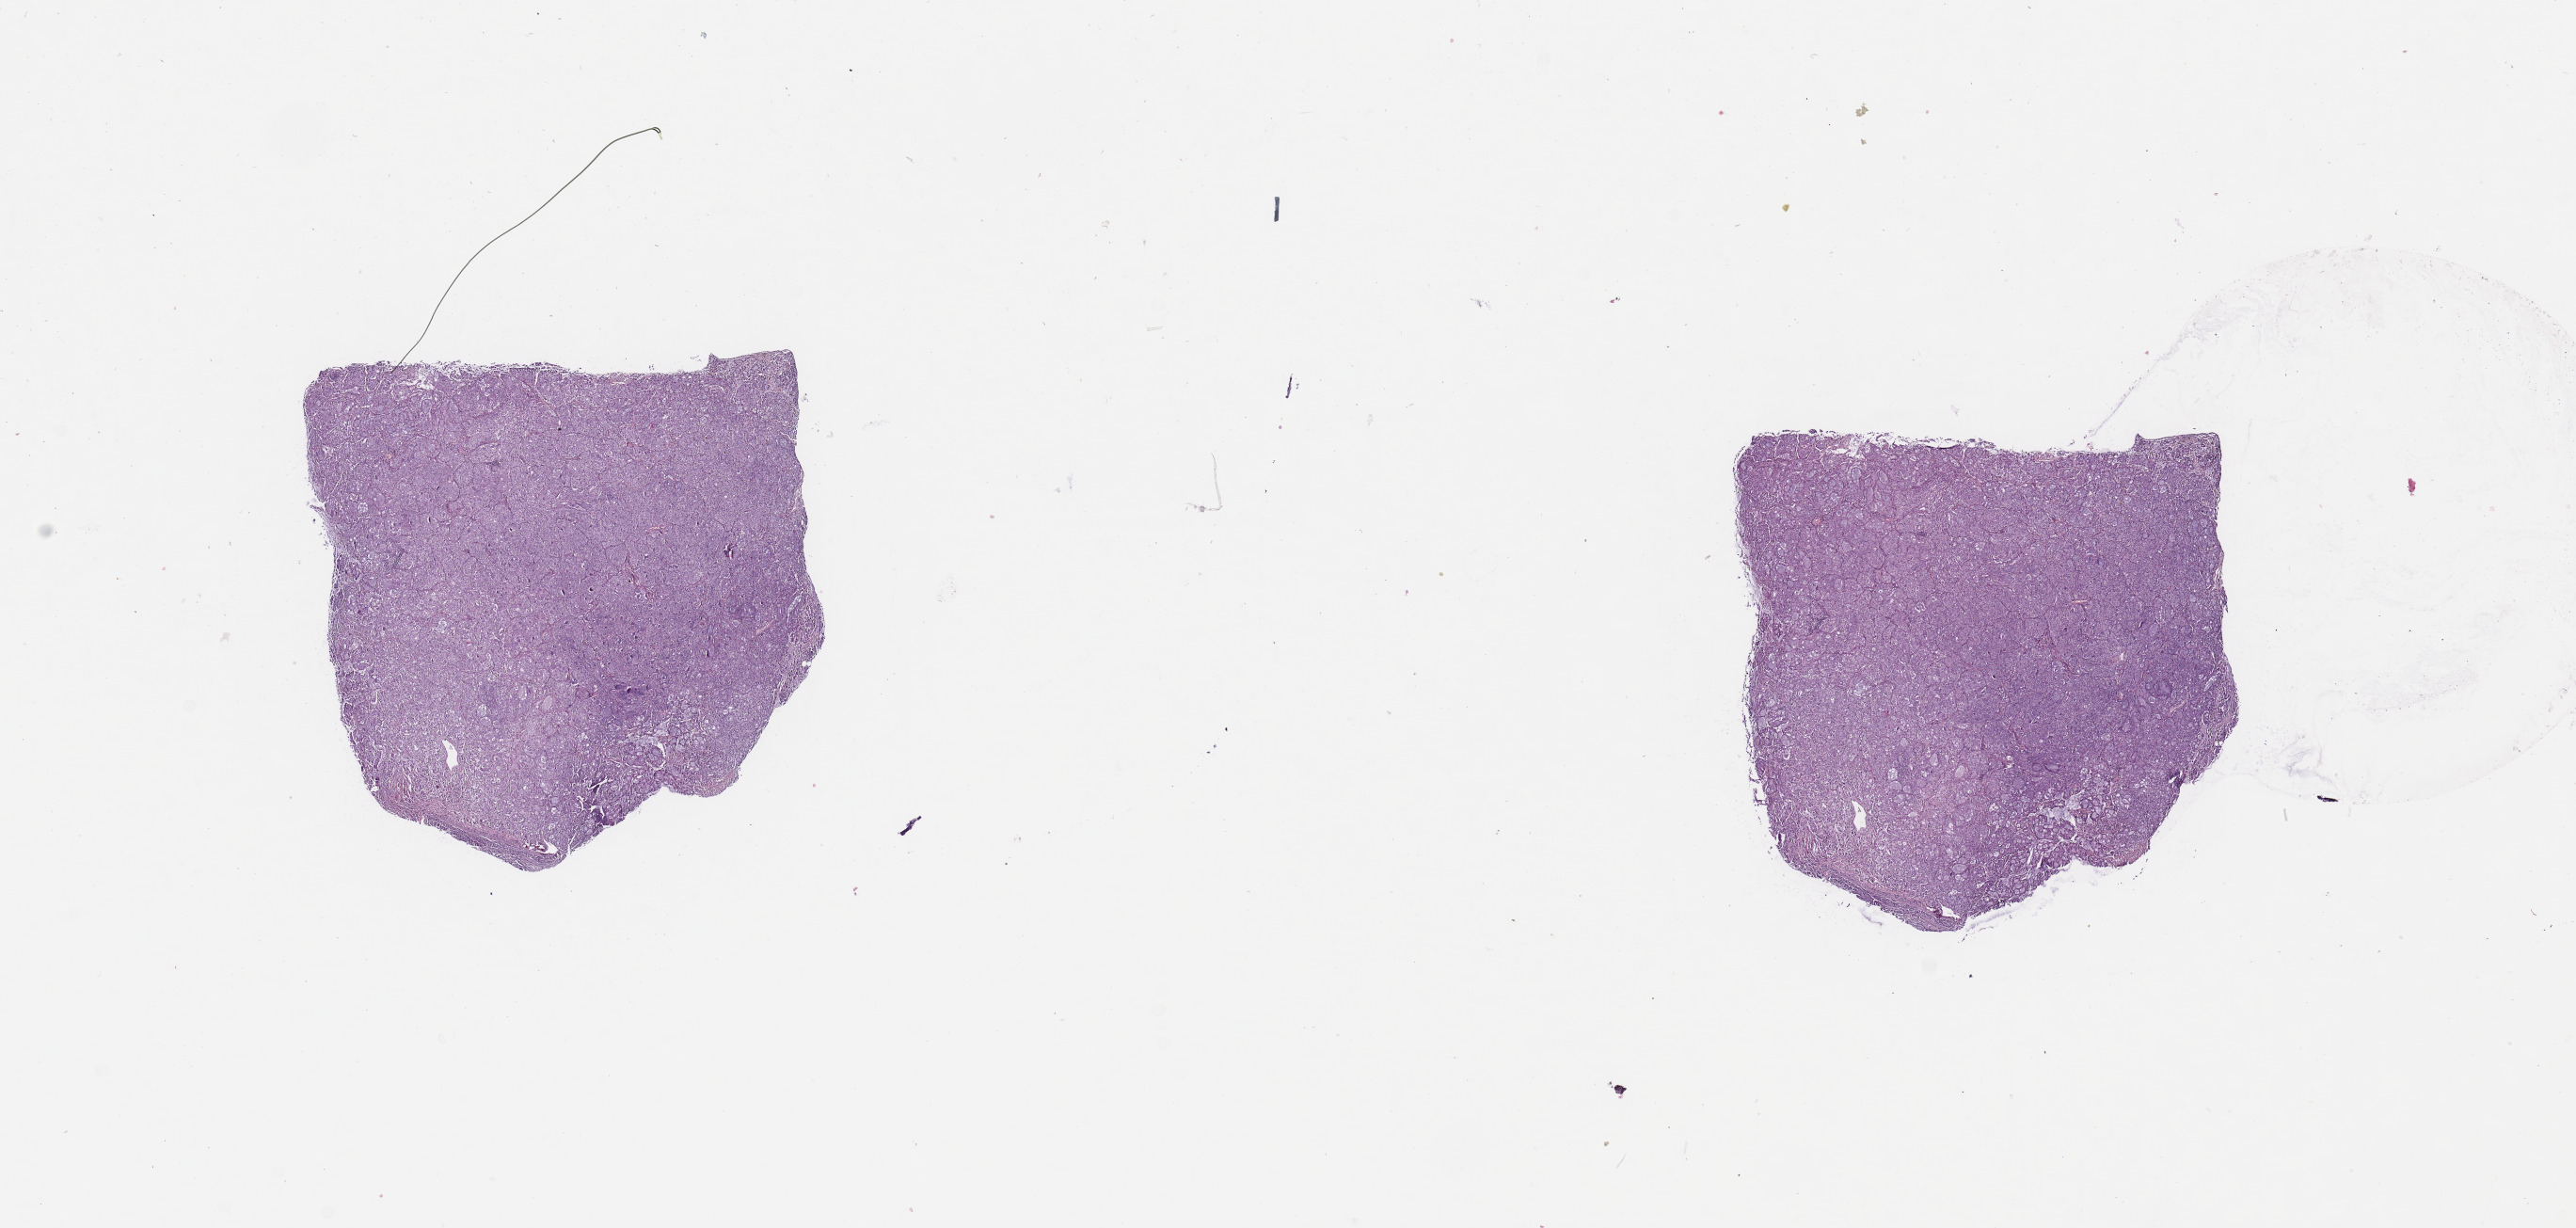
Hematoxylin and eosin (H&E) stained whole-slide image, shown as a low-resolution overview of the whole scanned area (about 21.7 x 10.3 mm, acquisition: 20x scan), tumour tissue sample, sampled site: lung. 51-year-old male patient. Histologic grade: G2 (moderately differentiated). Slide review estimates, as recorded: tumour nuclei 80%, necrosis 2%.
Diagnosis: Adenocarcinoma, NOS. AJCC pathologic stage: IIIA.